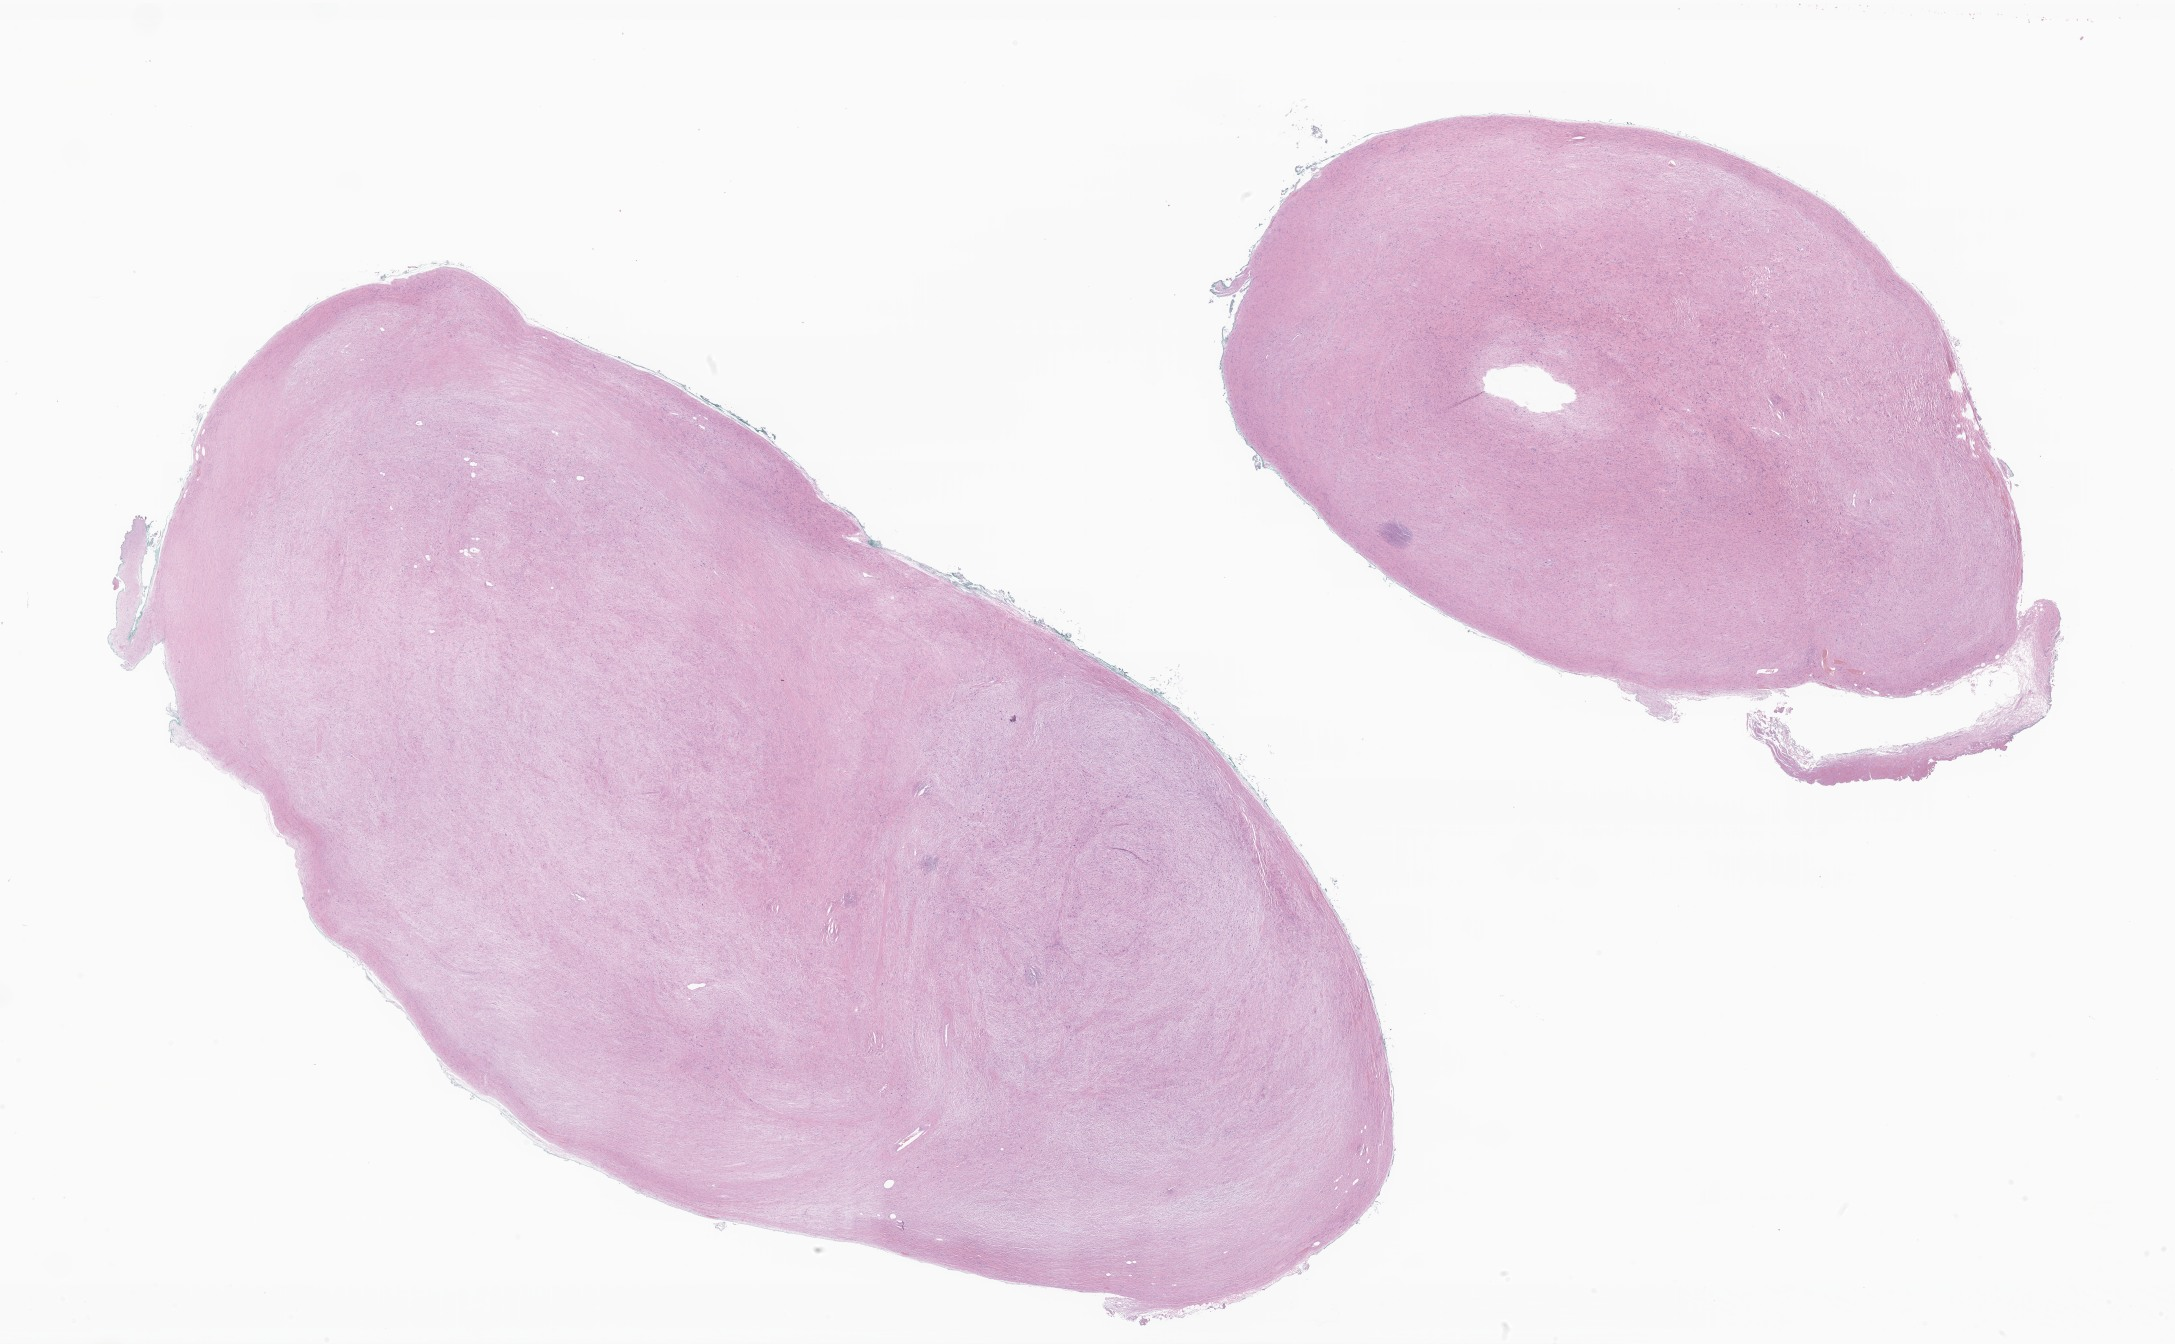
Digitized haematoxylin and eosin-stained section of tumor tissue from the soft tissue of upper extremity — a low-resolution overview of the entire scanned area, about 36.7 x 22.7 mm; FFPE section. Male patient, age 164 months.
Recorded diagnosis: Dedifferentiated liposarcoma.